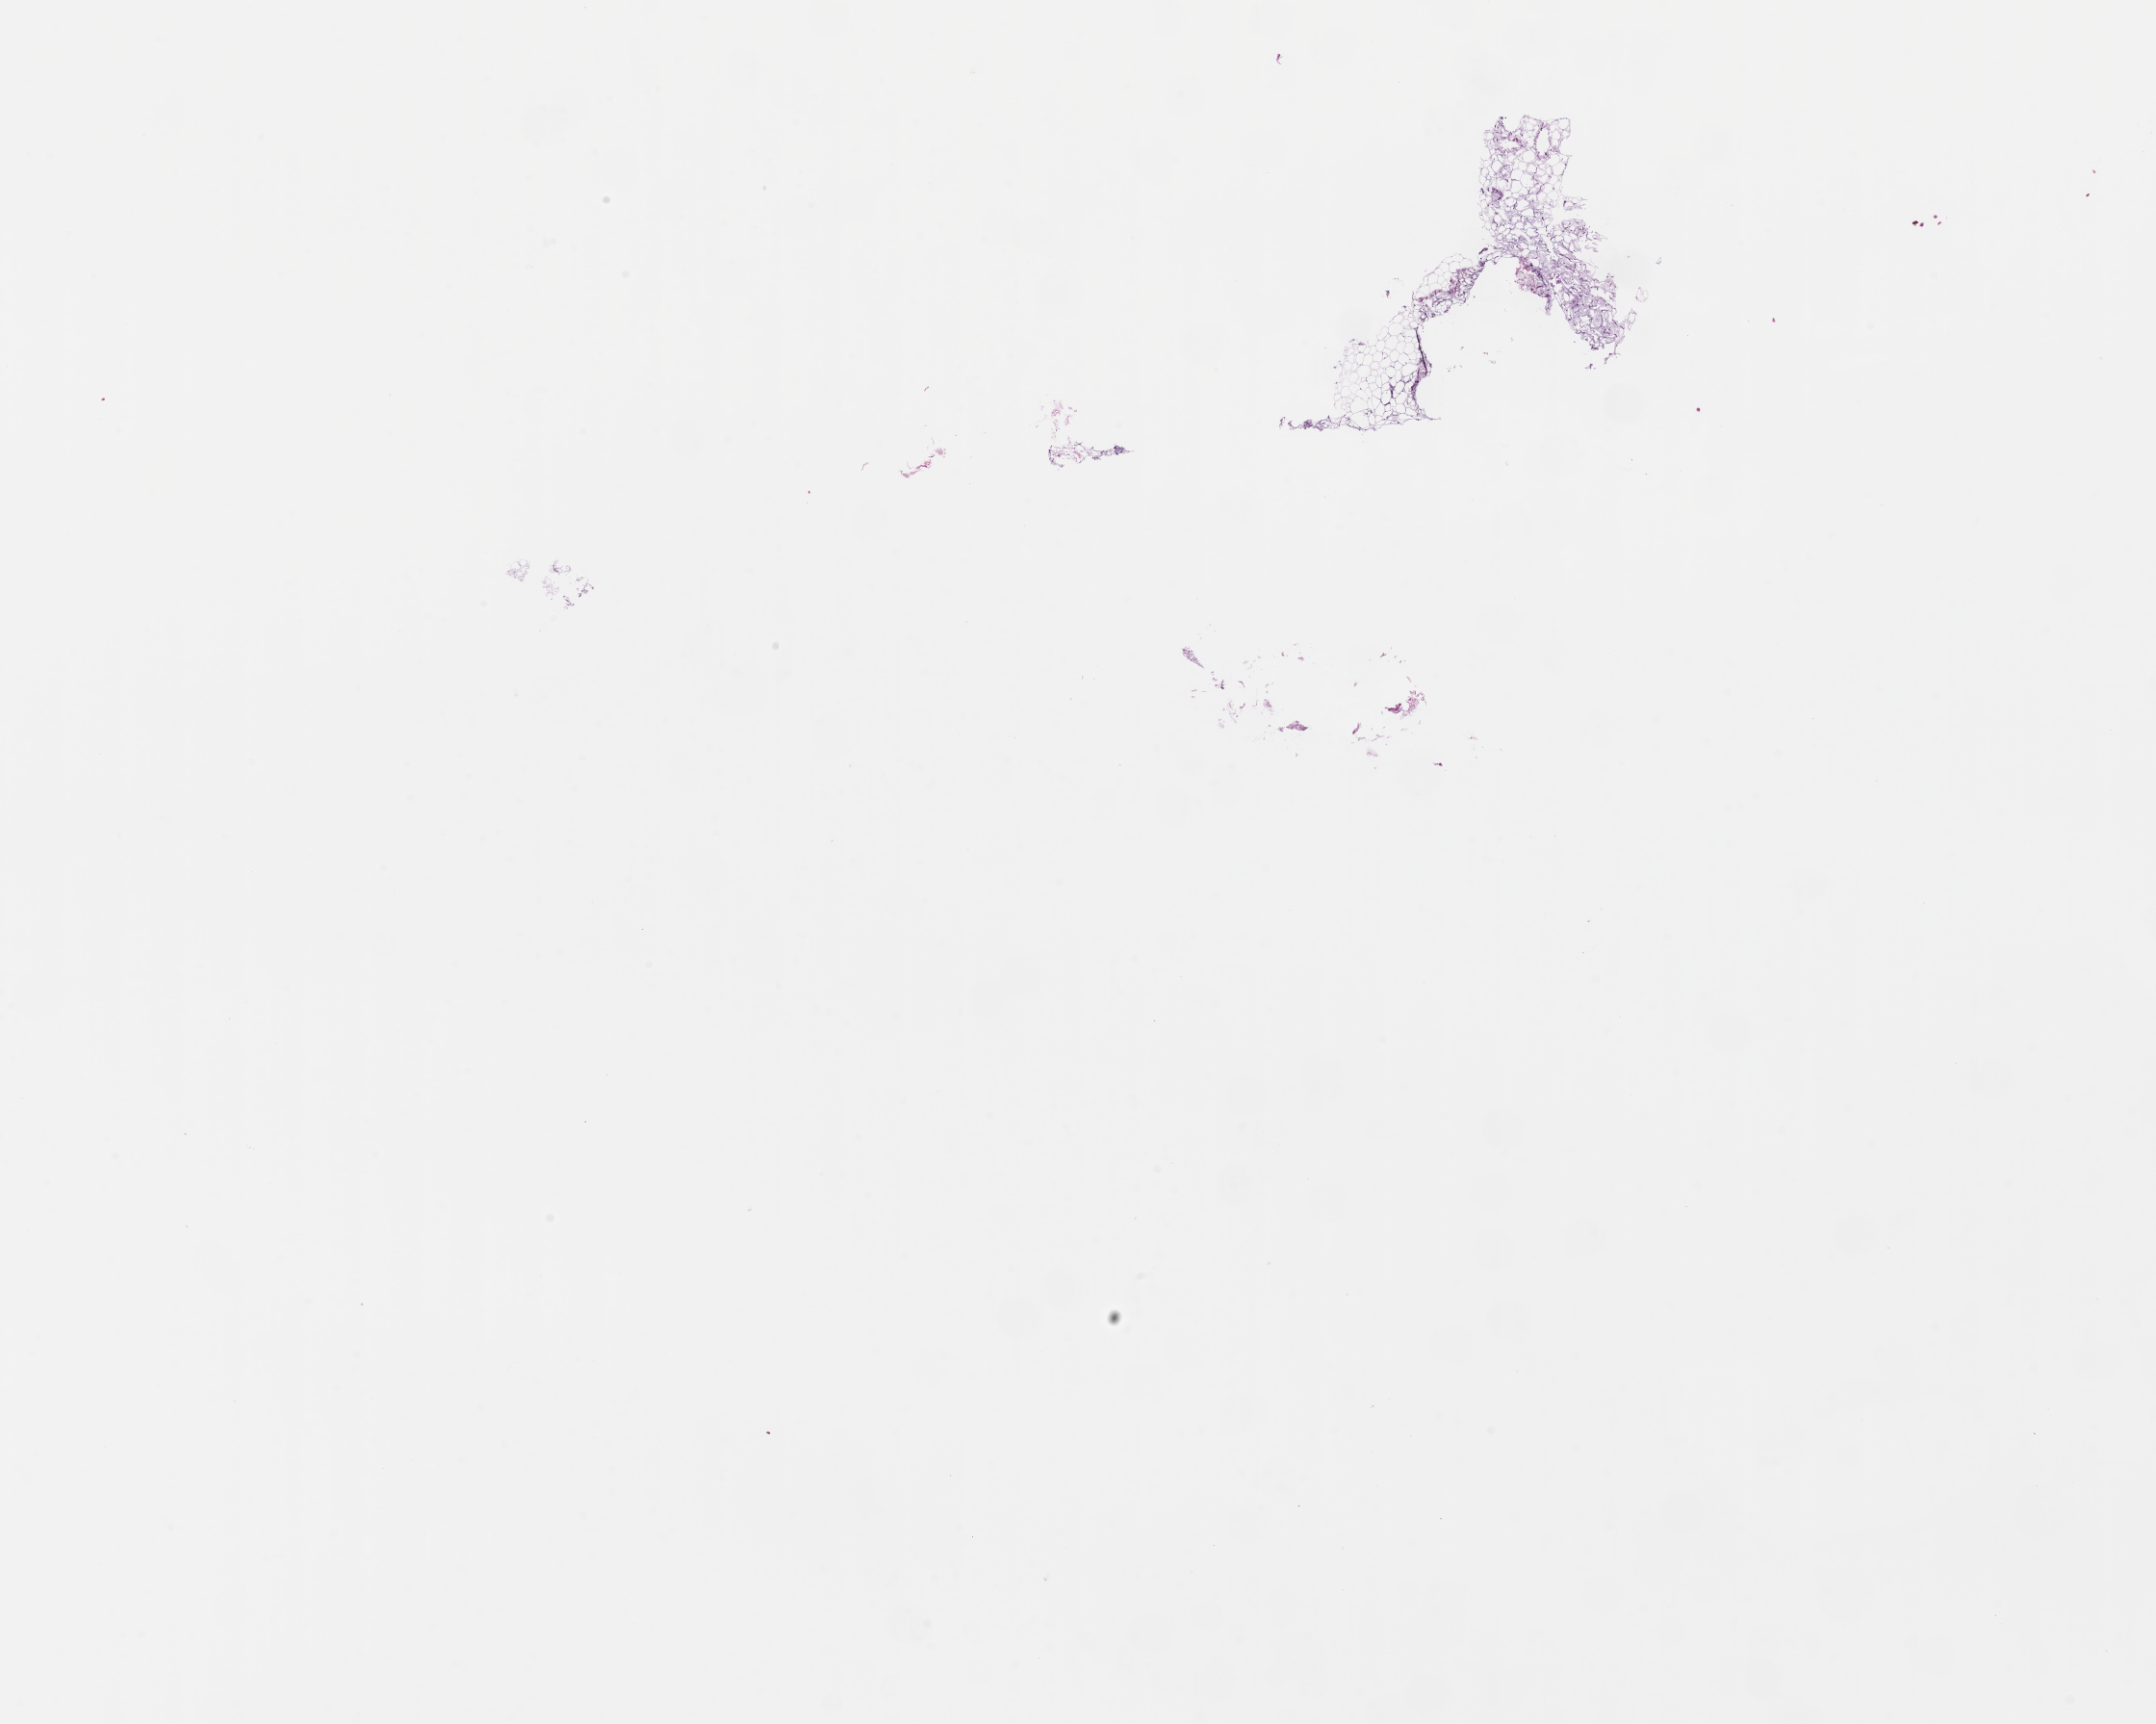
Whole-slide image, H&E stain, a low-resolution overview of the entire scanned area, about 18.1 x 14.5 mm, formalin-fixed, paraffin-embedded (FFPE) tissue. Patient: female.
This section: metastasis (sampled organ not recorded). Primary diagnosis of the patient: Melanoma.